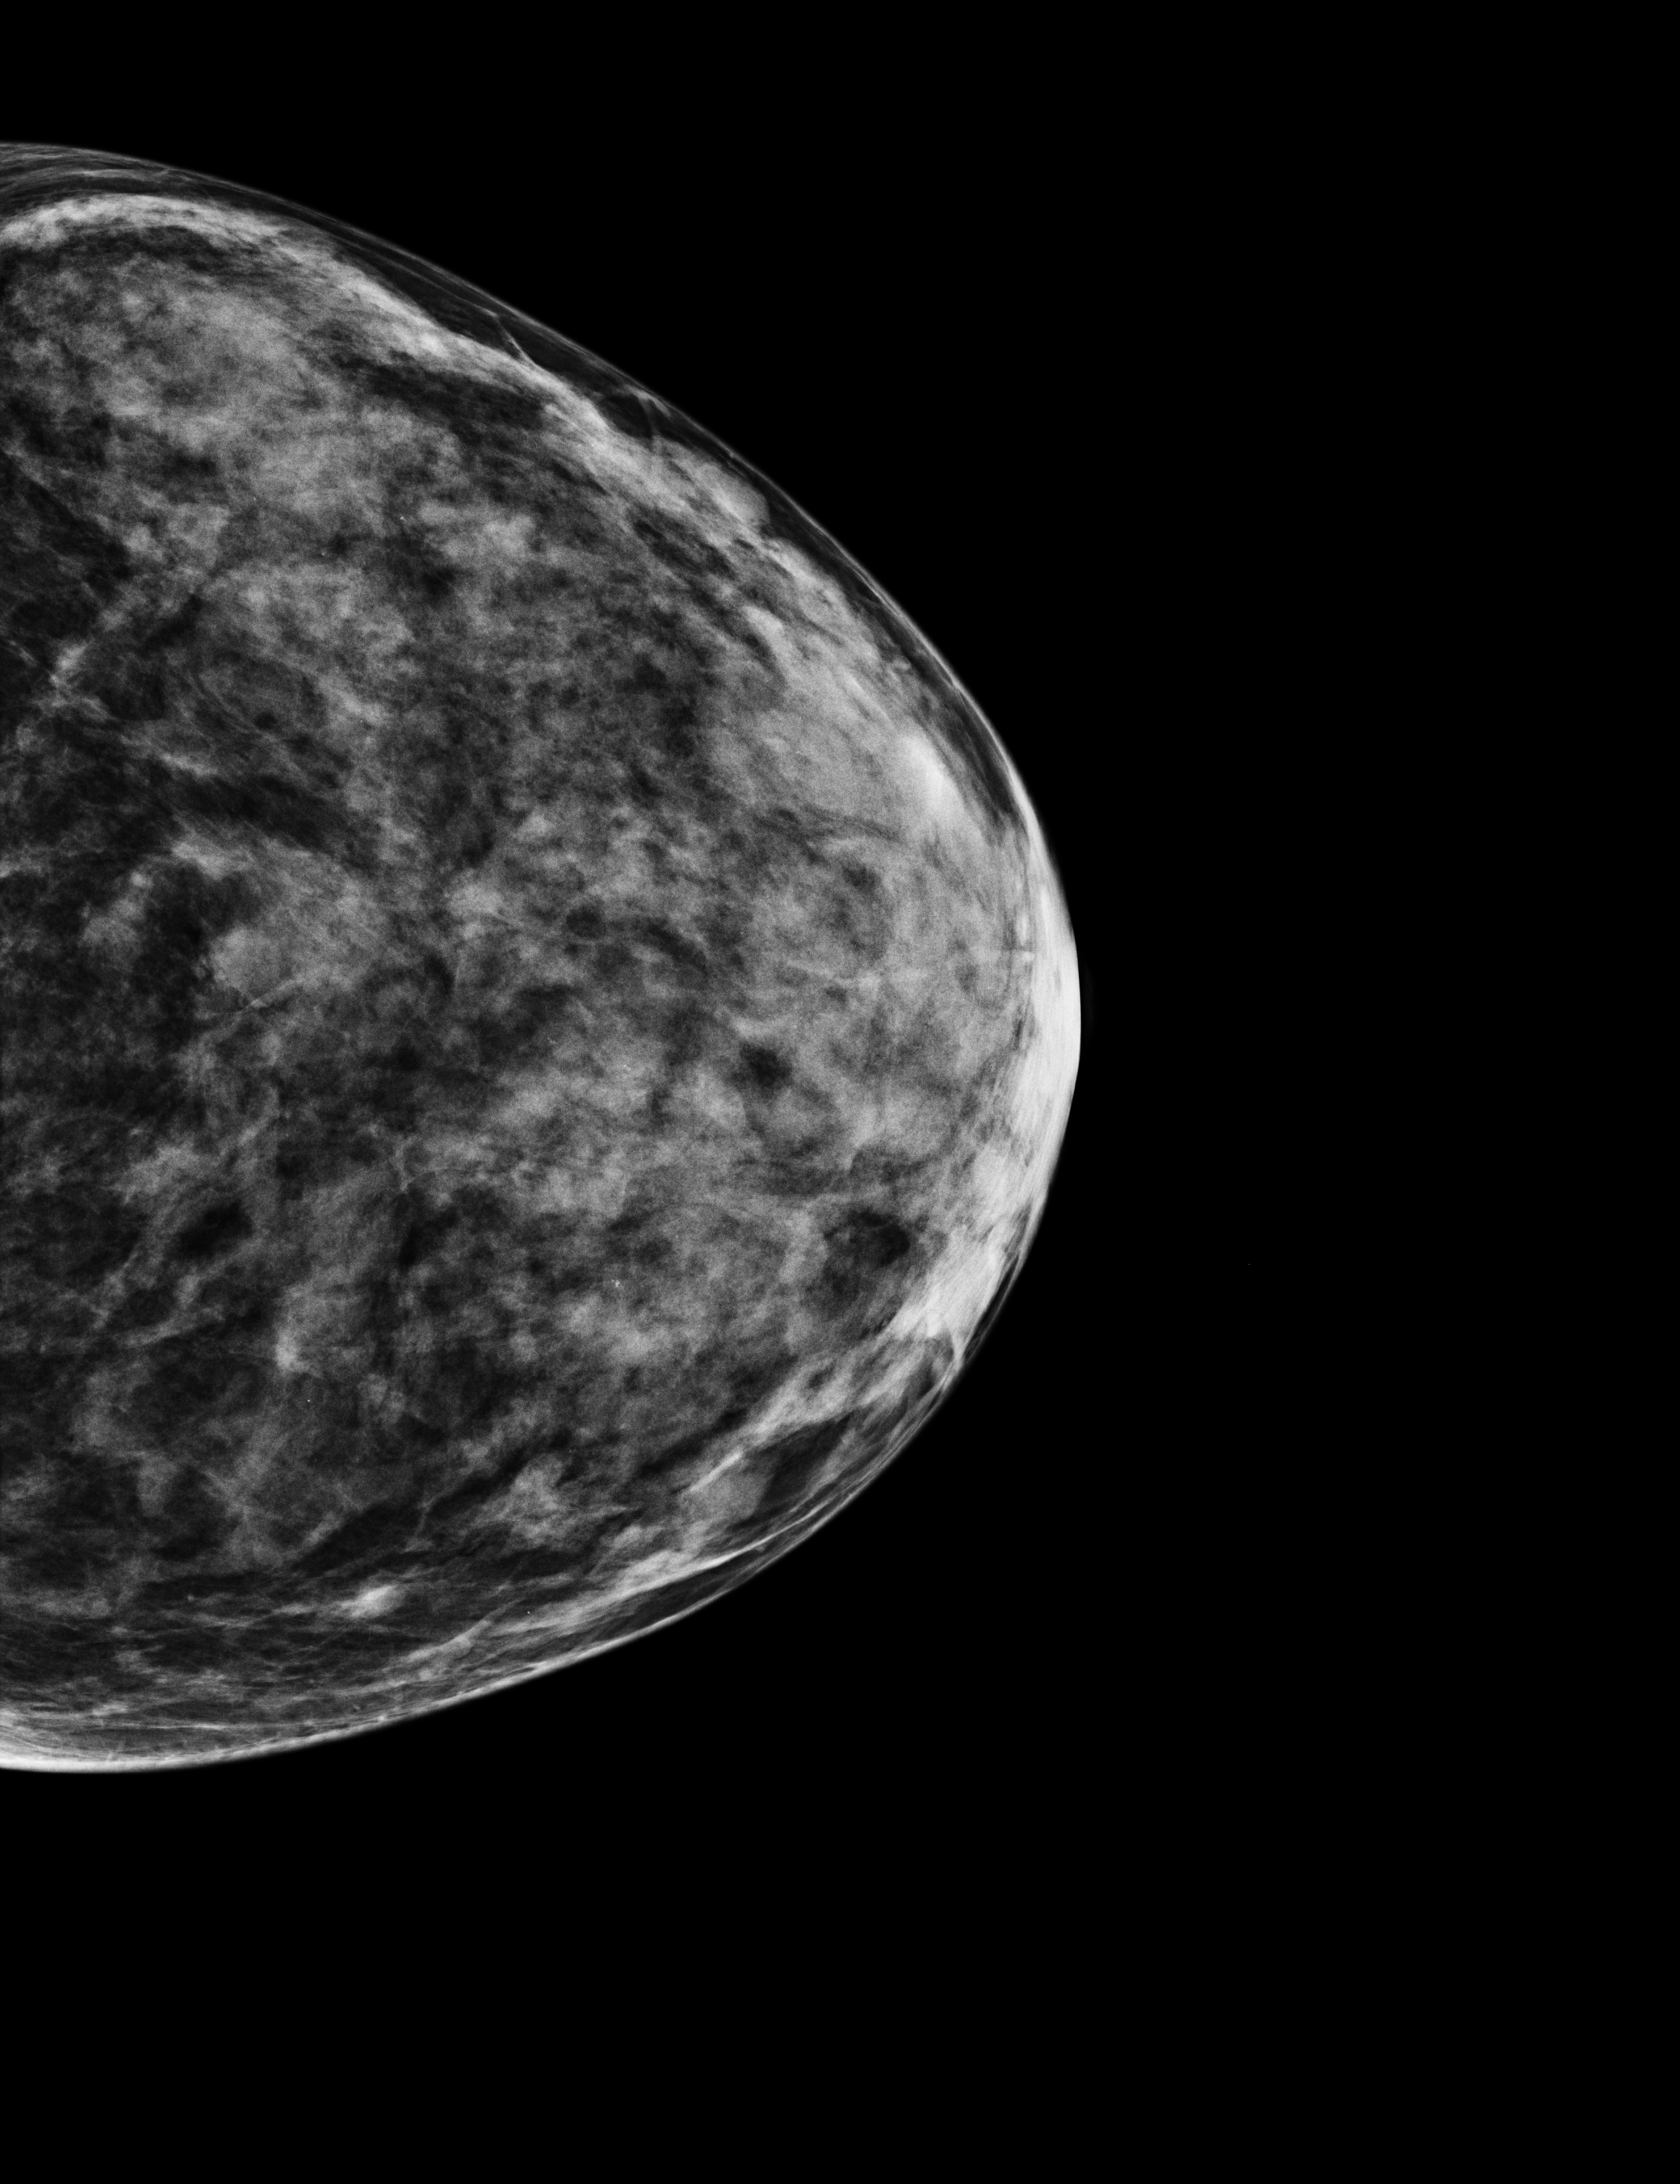
Digital mammogram (FFDM), left breast, CC view, annual screening mammography examination, compressed breast thickness 35 mm. Patient aged 43 years (female).
Breast density at the screening exam (both breasts): extremely dense (BI-RADS density category d).